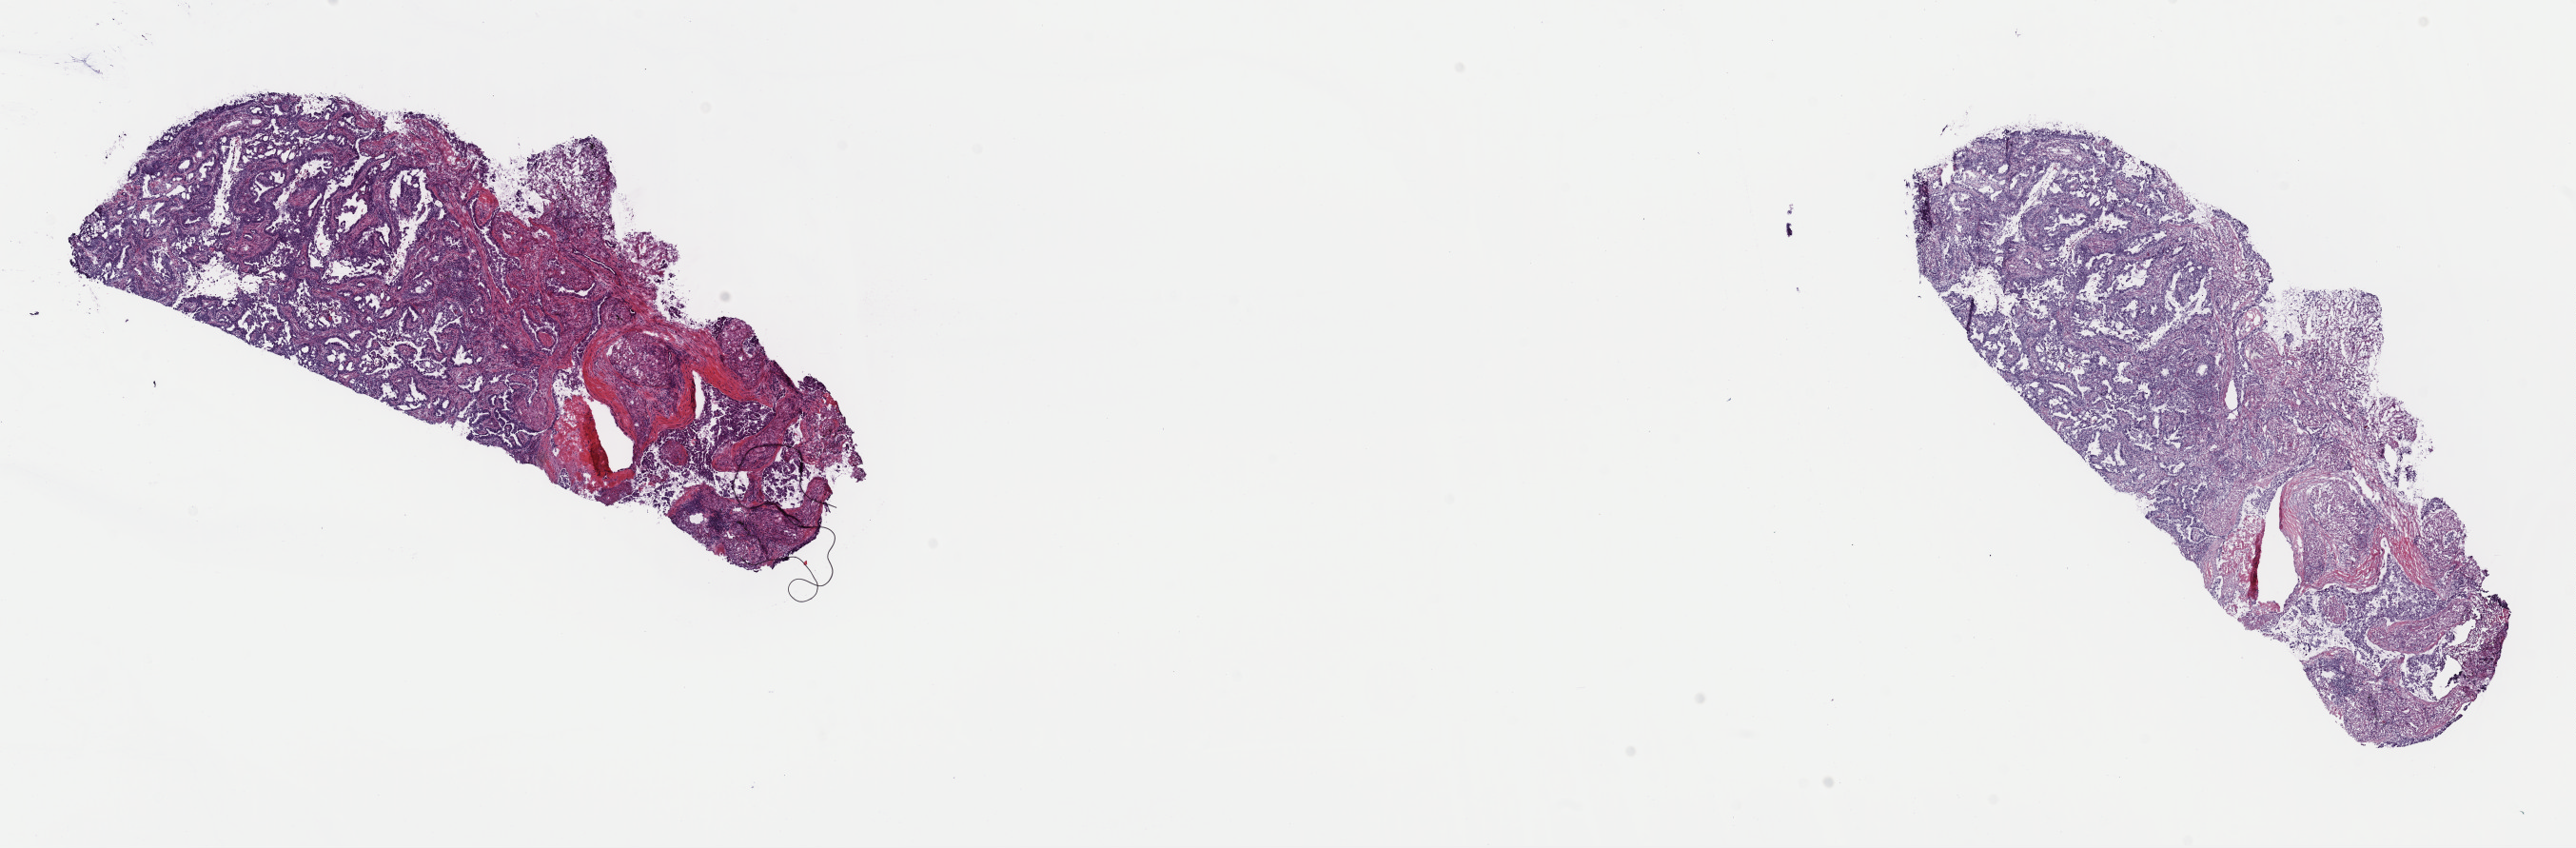
Whole-slide histology image, Hematoxylin and eosin (H&E) stained, whole scanned area (about 21.4 x 7.0 mm) shown as a low-resolution overview; frozen section; sample: primary tumour, lung. Patient: female, age at initial diagnosis 67 years. Composition of this section per pathologist review: tumour cells 70%, tumour nuclei 70%.
Diagnosis: Adenocarcinoma, NOS.